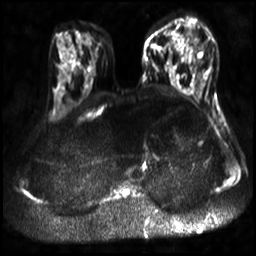
Breast MRI, one axial slice. Slice 13 of 30 in the series (ordered by position). Diffusion-weighted series; image 2 of 4 stored at this slice position (different b-values; order by instance number). 3 T. 4 mm slice thickness. 256 × 256 image matrix, field of view 320 × 320 mm. Female patient.
Structures marked on this image (expert manual segmentation):
- tumour on diffusion-weighted imaging: bounding box (x1, y1, x2, y2) in pixels: (191, 34, 203, 44)